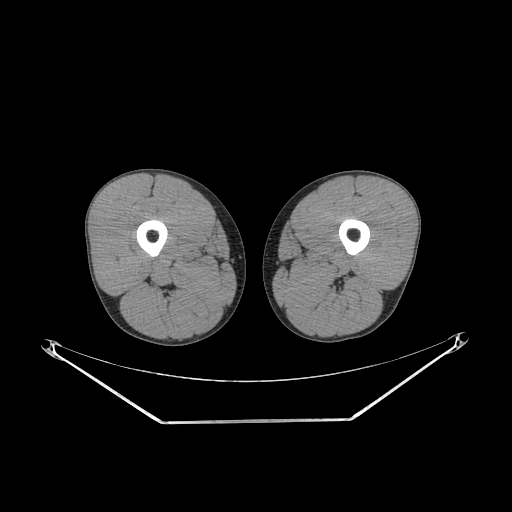
CT of an extremity soft-tissue mass (from a PET/CT study), one axial slice; slice 218 of 267 in the series (ordered by position); reconstruction kernel SOFT; soft-tissue window (W 400 / L 40 HU); 3.75 mm slice thickness; 512 × 512 image matrix, field of view 500 × 500 mm. Male patient. Case-level facts recorded for this patient, not image findings: histological type: extraskeletal osteosarcoma; grade: high; site of the primary tumour: left adductur.
Annotated regions visible in this slice (expert contour drawn on MRI and transferred to this co-registered scan by the dataset authors):
- gross tumour volume (mass): bounding box <285,251,355,280> (left, top, right, bottom; pixels)